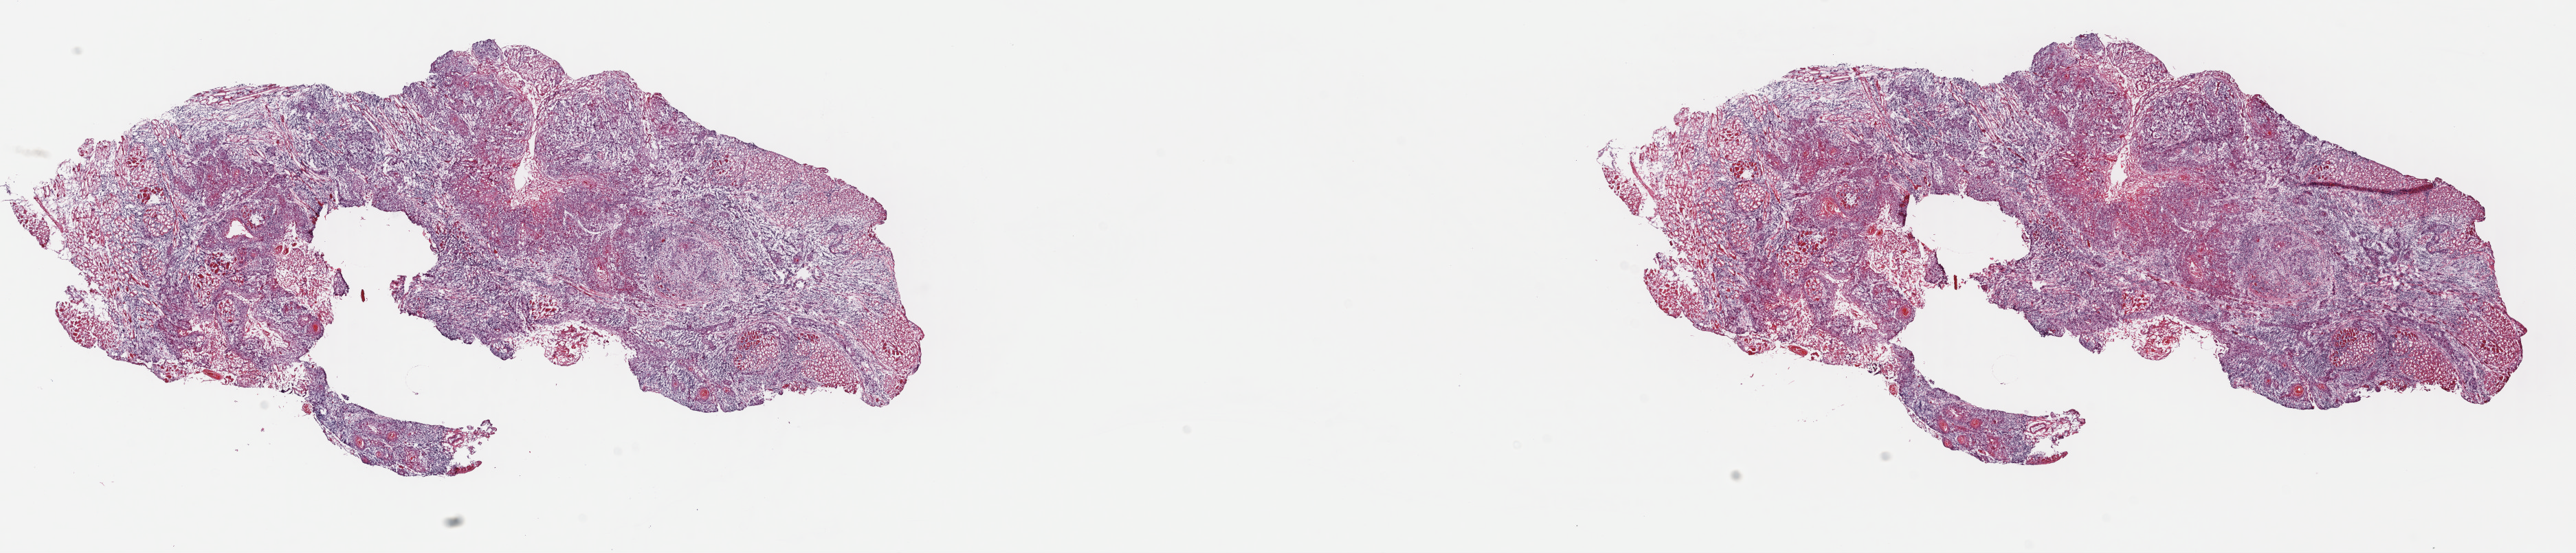
Digitized H&E-stained tissue section (whole slide) — a low-resolution overview of the entire scanned area, about 29.5 x 6.3 mm; frozen section from the top of the tissue portion; primary tumour sample from the head and neck. Female, age 35 years at initial diagnosis. Histologic grade: G2 (moderately differentiated). Slide review estimates, as recorded: tumour cells 80%, tumour nuclei 80%, normal cells 0%, stromal cells 10%, necrosis 10%. Infiltration values recorded for this section: lymphocyte infiltration 40%, monocyte infiltration 20%, neutrophil infiltration 20%.
- histologic diagnosis: Squamous cell carcinoma, keratinizing, NOS (tongue, NOS)
- laterality: left
- TNM: T2 N2b M0
- AJCC pathologic stage: IVA